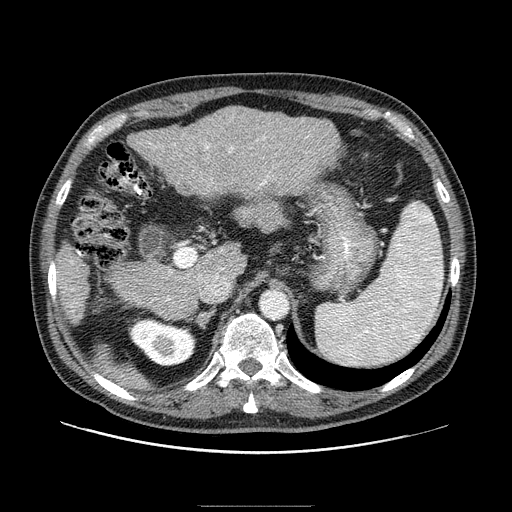
Contrast-enhanced abdominal CT (liver protocol), one axial slice. Slice 52 of 99 in the series (ordered by position). 100 kVp. One of 2 acquisitions stored at this slice position. Soft-tissue window (W 400 / L 40 HU). 2.5 mm slice thickness. 512 × 512 image matrix, field of view 400 × 400 mm. Case-level facts recorded for this patient, not image findings: diagnosis: hepatocellular carcinoma (patient treated with transarterial chemoembolisation; whether this scan precedes or follows treatment is not stated here); TNM stage (as recorded): Stage-II; Child-Pugh class: A; tumour differentiation: well differentiated; tumour nodularity: multinodular.
Annotated regions visible in this slice (semi-automatically segmented with operator editing):
- liver parenchyma outside the tumour (the mass and vessels are separate outlines, so this box may not span the whole liver): bounding box [x1, y1, x2, y2] px = [55, 106, 340, 324]
- liver vessels: [70, 136, 269, 307]